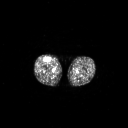
FDG PET of an extremity soft-tissue mass (from a PET/CT study), one axial slice; slice 243 of 311 in the series (ordered by position); 128 × 128 image matrix. Male patient, age 56 years. Case-level facts recorded for this patient, not image findings: histological type: pleiomorphic leiomyosarcoma; grade: intermediate; site of the primary tumour: right thigh.
Annotated regions visible in this slice (expert contour drawn on MRI and transferred to this co-registered scan by the dataset authors):
- gross tumour volume including surrounding oedema: bounding box [x1, y1, x2, y2] px = [45, 57, 51, 62]